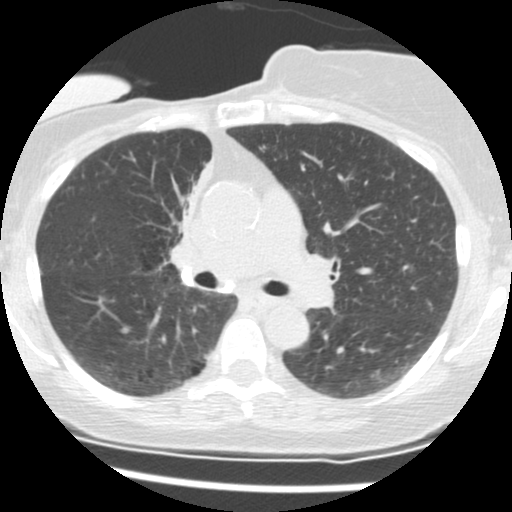
Low-dose screening chest CT, axial slice; second annual screen; lung window (W 1500 / L -600 HU); 2.5 mm slice thickness; standard (soft-tissue) reconstruction kernel (STANDARD); slice 56 of 165 in the series. Female, age 56 years at enrolment. Current smoker at enrolment.
- Expert reader's lesion annotation, bounding box <152,158,207,254> (left, top, right, bottom; pixels).
- The screening reader recorded 2 non-calcified nodules or masses ≥4 mm on this exam (right middle lobe, right lower lobe); which of them this box marks is not recorded.
- Official screen result: positive, change unspecified: nodule(s) >= 4 mm or enlarging nodule(s), mass(es), or other non-specific abnormalities suspicious for lung cancer.
- Participant outcome: lung cancer diagnosed 675 days after this screen (after the third annual screen) — adenocarcinoma, NOS, right upper lobe, stage IIIB (AJCC 6th edition), 8 mm at pathology.